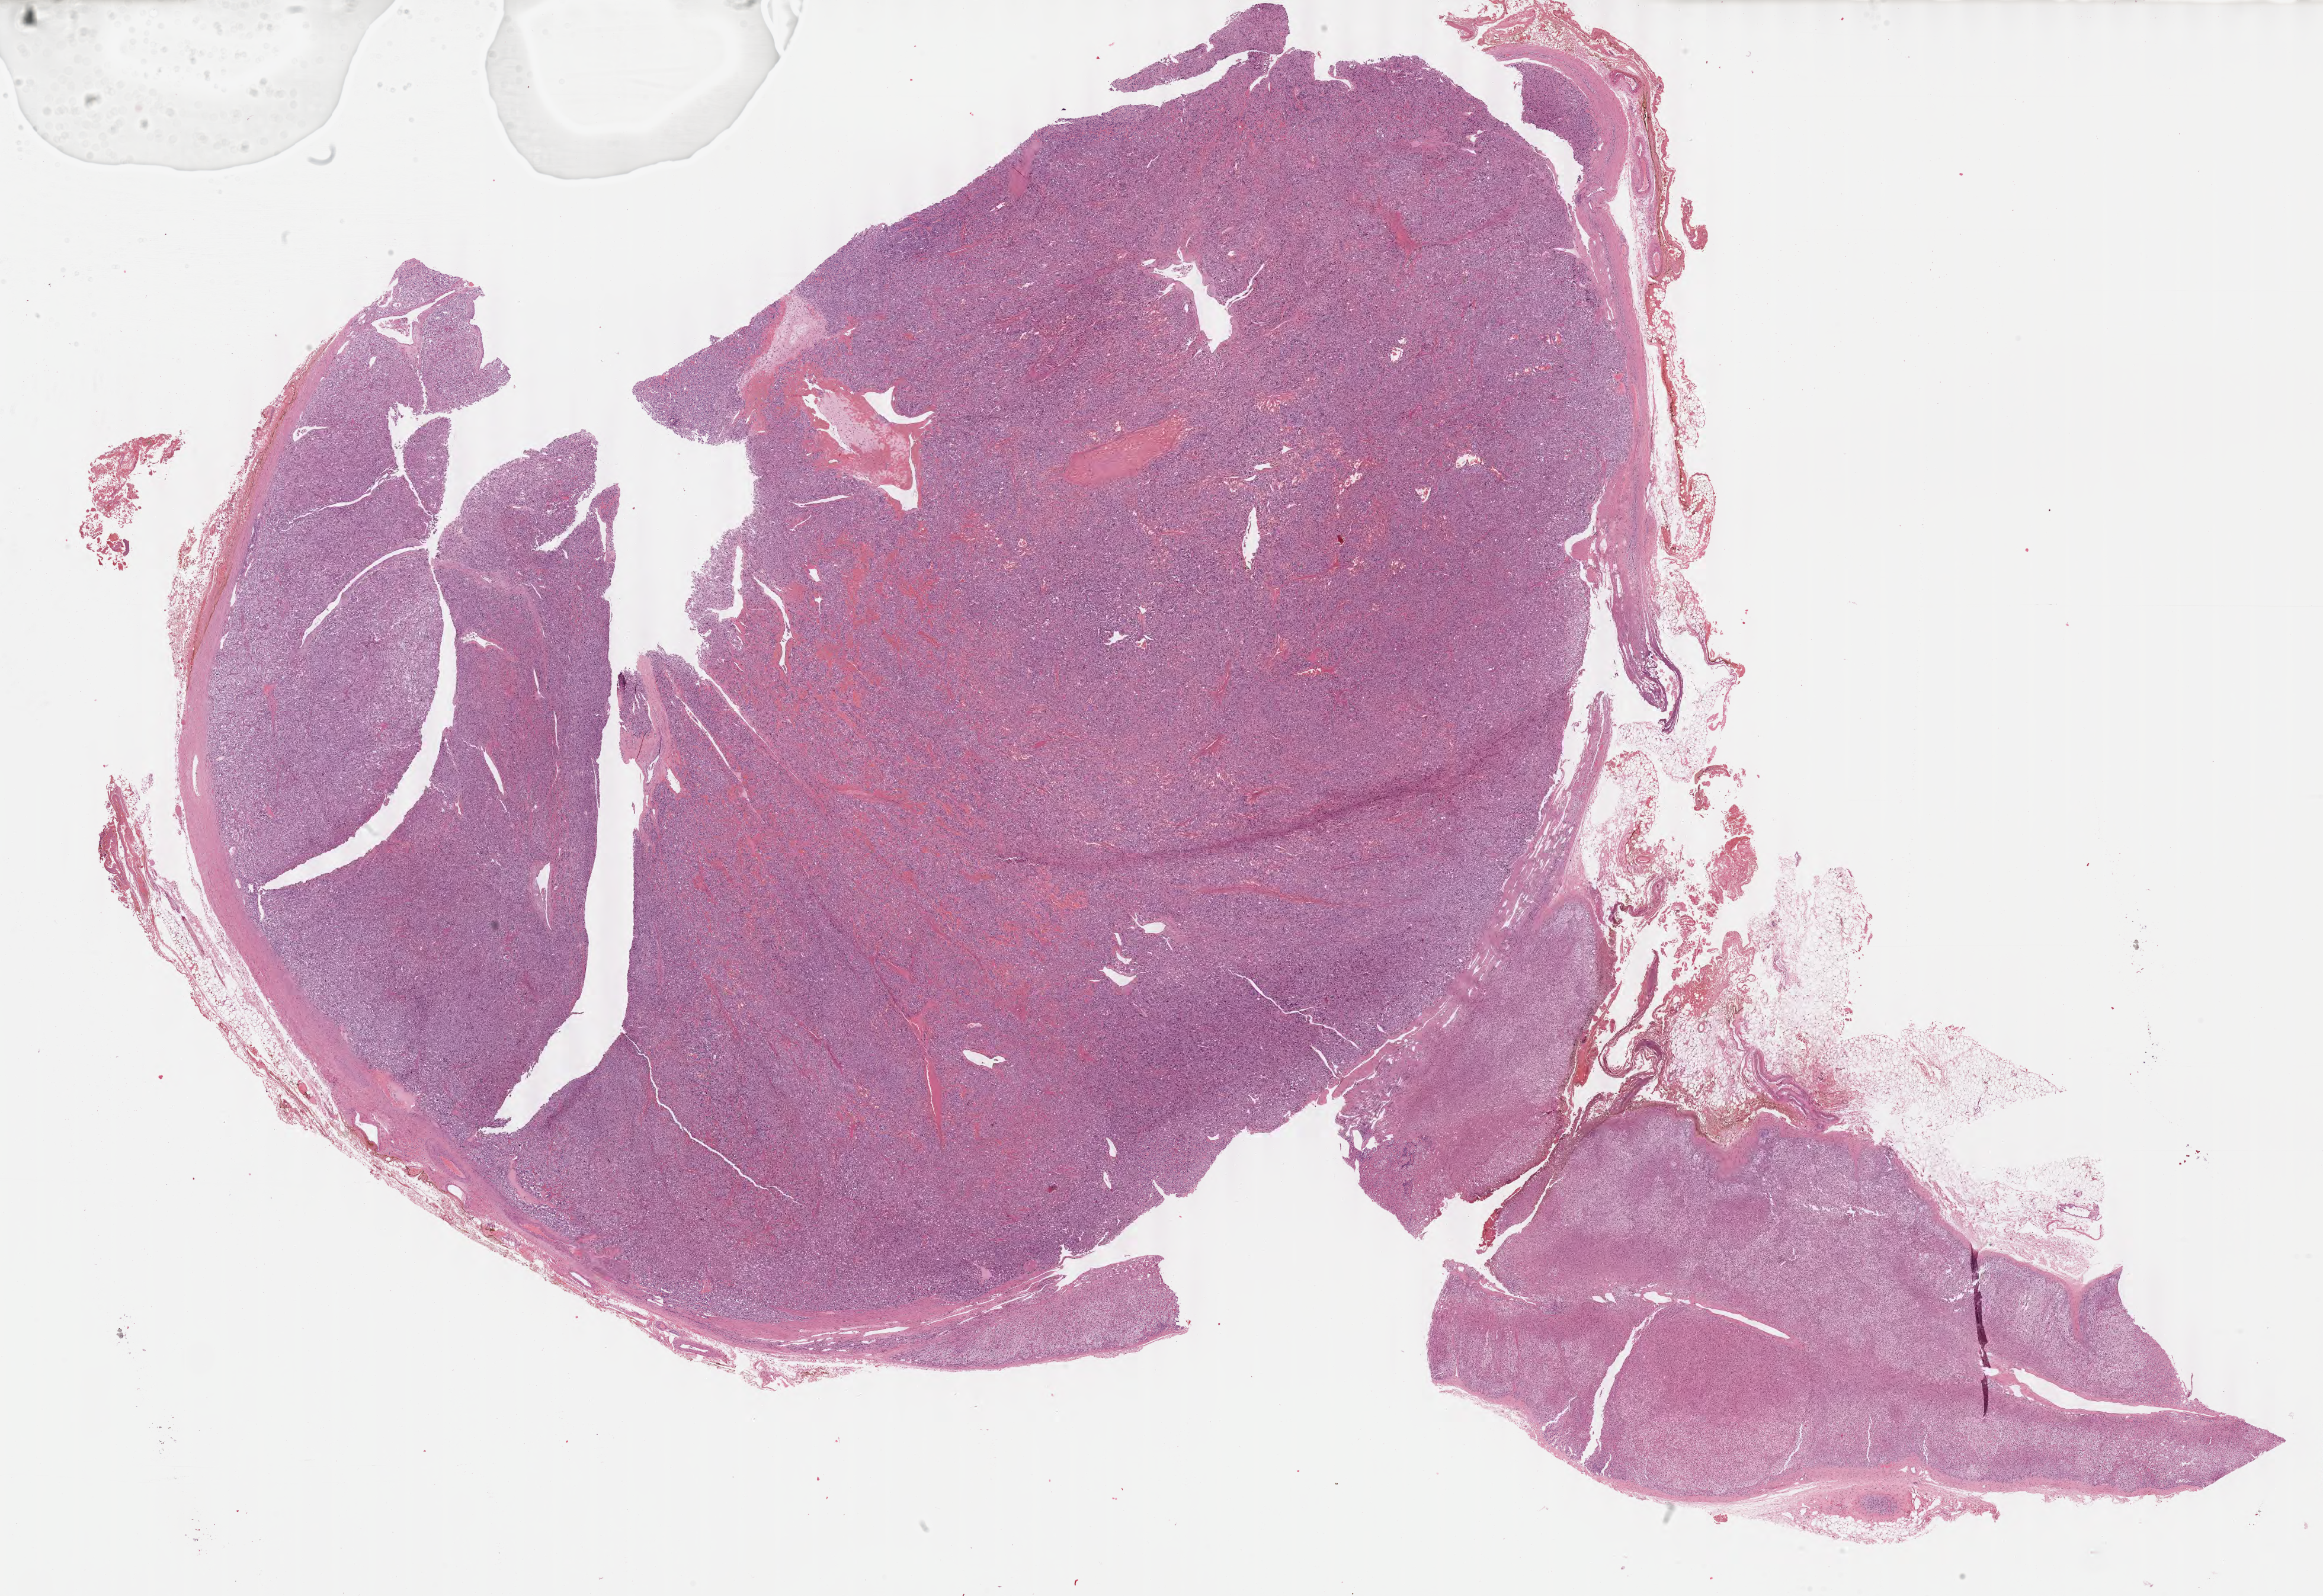
Hematoxylin and eosin (H&E) stained whole-slide image, a low-resolution overview of the entire scanned area, about 31.0 x 21.3 mm (acquisition: 40x scan). Formalin-fixed paraffin-embedded (FFPE) diagnostic section. Adrenal gland, primary tumour sample. Male patient; age at initial diagnosis 26 years.
Laterality: right. Pathologic diagnosis: Pheochromocytoma, NOS.